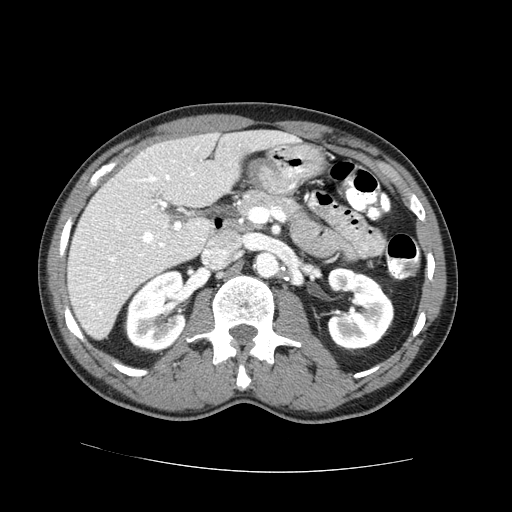
Contrast-enhanced abdominal CT (liver protocol), one axial slice. Slice 34 of 73 in the series (ordered by position). One of 2 acquisitions stored at this slice position. Soft-tissue window (W 400 / L 40 HU). 512 × 512 image matrix, field of view 380 × 380 mm. From the clinical record (not read from this slice): diagnosis: hepatocellular carcinoma (patient treated with transarterial chemoembolisation; whether this scan precedes or follows treatment is not stated here); TNM stage (as recorded): Stage-IVA; Child-Pugh class: A; tumour differentiation: no biopsy.
Outlined on this slice (semi-automatic segmentation, software-assisted and operator-edited):
- liver parenchyma outside the tumour (the mass and vessels are separate outlines, so this box may not span the whole liver): box from (x=66, y=130) to (x=298, y=338) px
- liver vessels: (x=90, y=138)–(x=294, y=307)